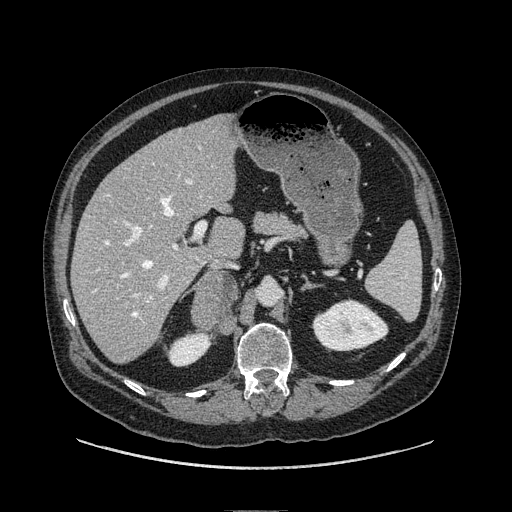
Contrast-enhanced abdominal CT, one axial slice. Slice 52 of 149 in the series (ordered by position). Soft-tissue window (W 400 / L 40 HU). 512 × 512 image matrix, field of view 440 × 440 mm. Male patient. From the clinical record (not read from this slice): diagnosis: adrenocortical carcinoma; tumour side: right adrenal; tumour size at pathology: 7.5 cm; Ki-67 index: 15 %; stage (as recorded): 2.
Outlined on this slice (semi-automatically segmented with operator editing):
- mass: bounding box <190,275,237,330> (left, top, right, bottom; pixels)